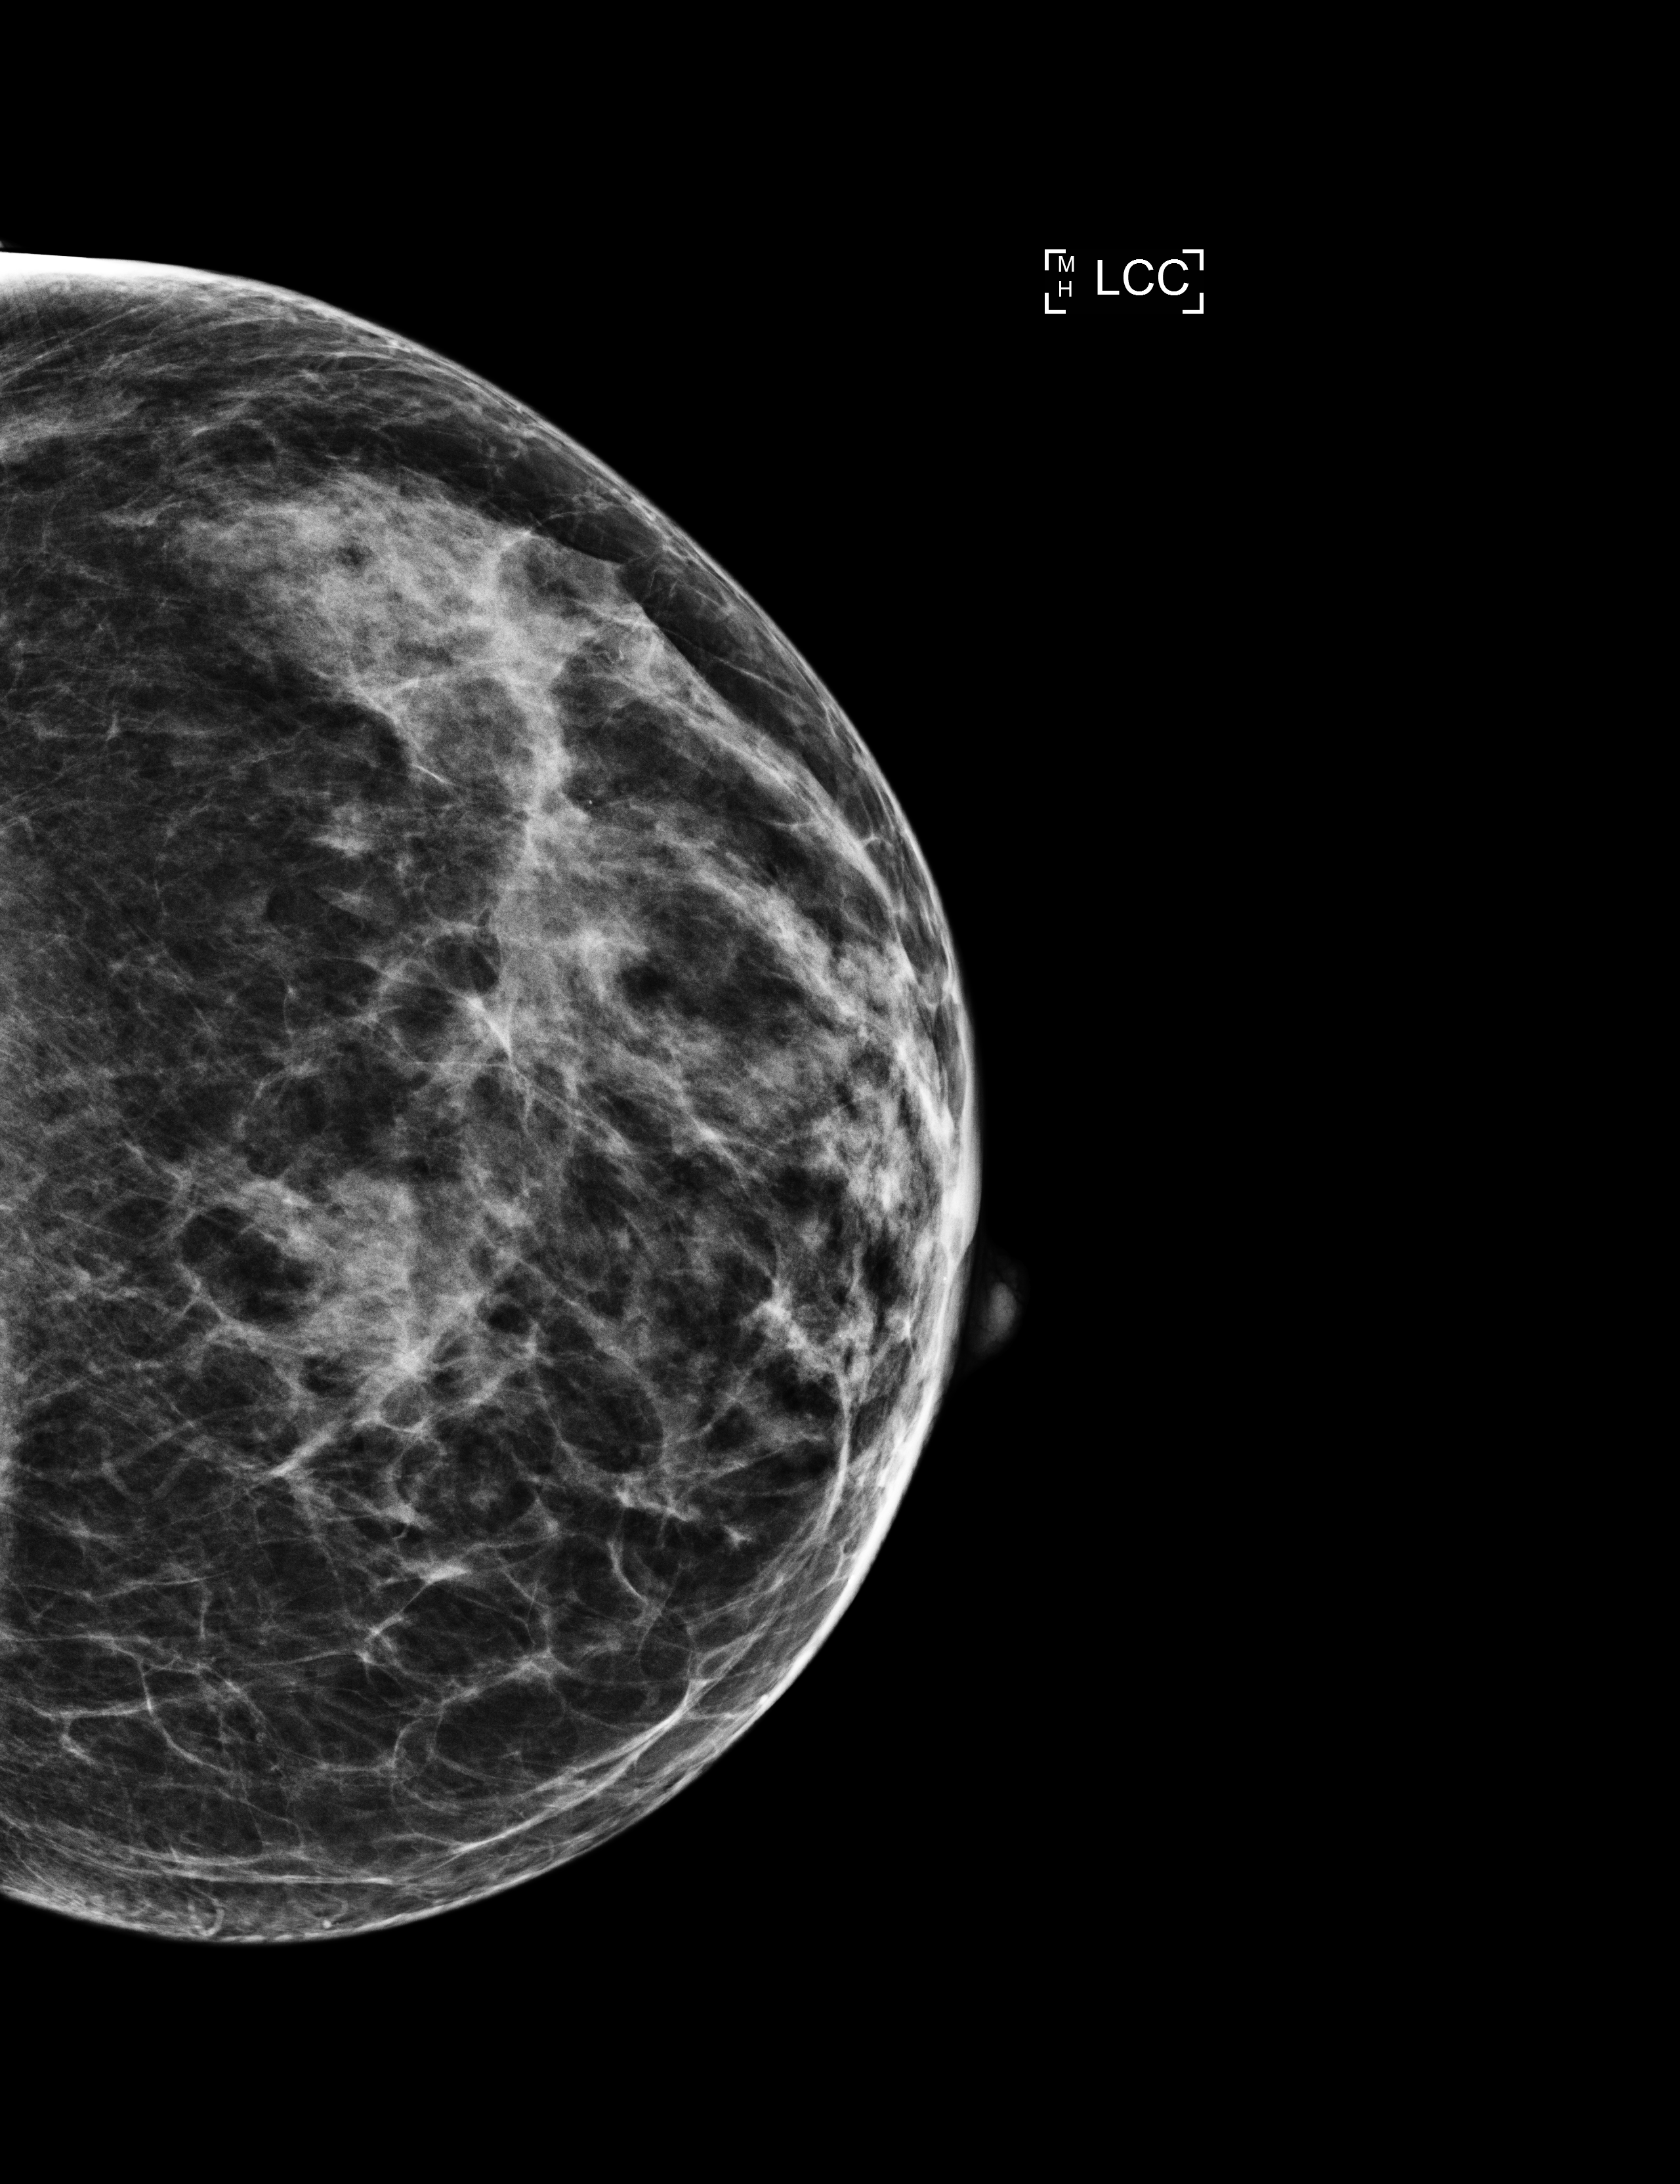
Screening examination; system: Selenia Dimensions.
Image type: full-field digital mammogram. Breast: left. Projection: CC view.